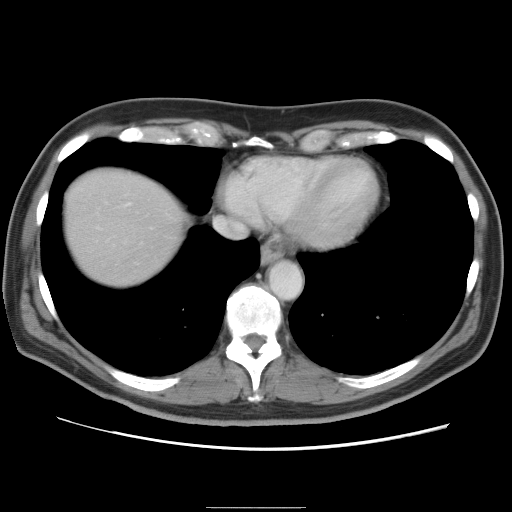
Contrast-enhanced abdominal CT, one axial slice; slice 77 of 87 in the series (ordered by position); 120 kVp; intravenous contrast given; soft-tissue window (W 400 / L 40 HU); 5 mm slice thickness; 512 × 512 image matrix. Male patient, age 63 years. Case-level facts recorded for this patient, not image findings: diagnosis: colorectal cancer liver metastases, imaged before liver resection; multiple liver metastases: no; largest metastasis: 9 cm; disease in both lobes: no.
Structures marked on this image (expert manual segmentation):
- liver: box from (x=64, y=170) to (x=183, y=286) px
- planned liver remnant (the part of the liver to remain after resection): (x=64, y=182)–(x=182, y=286)